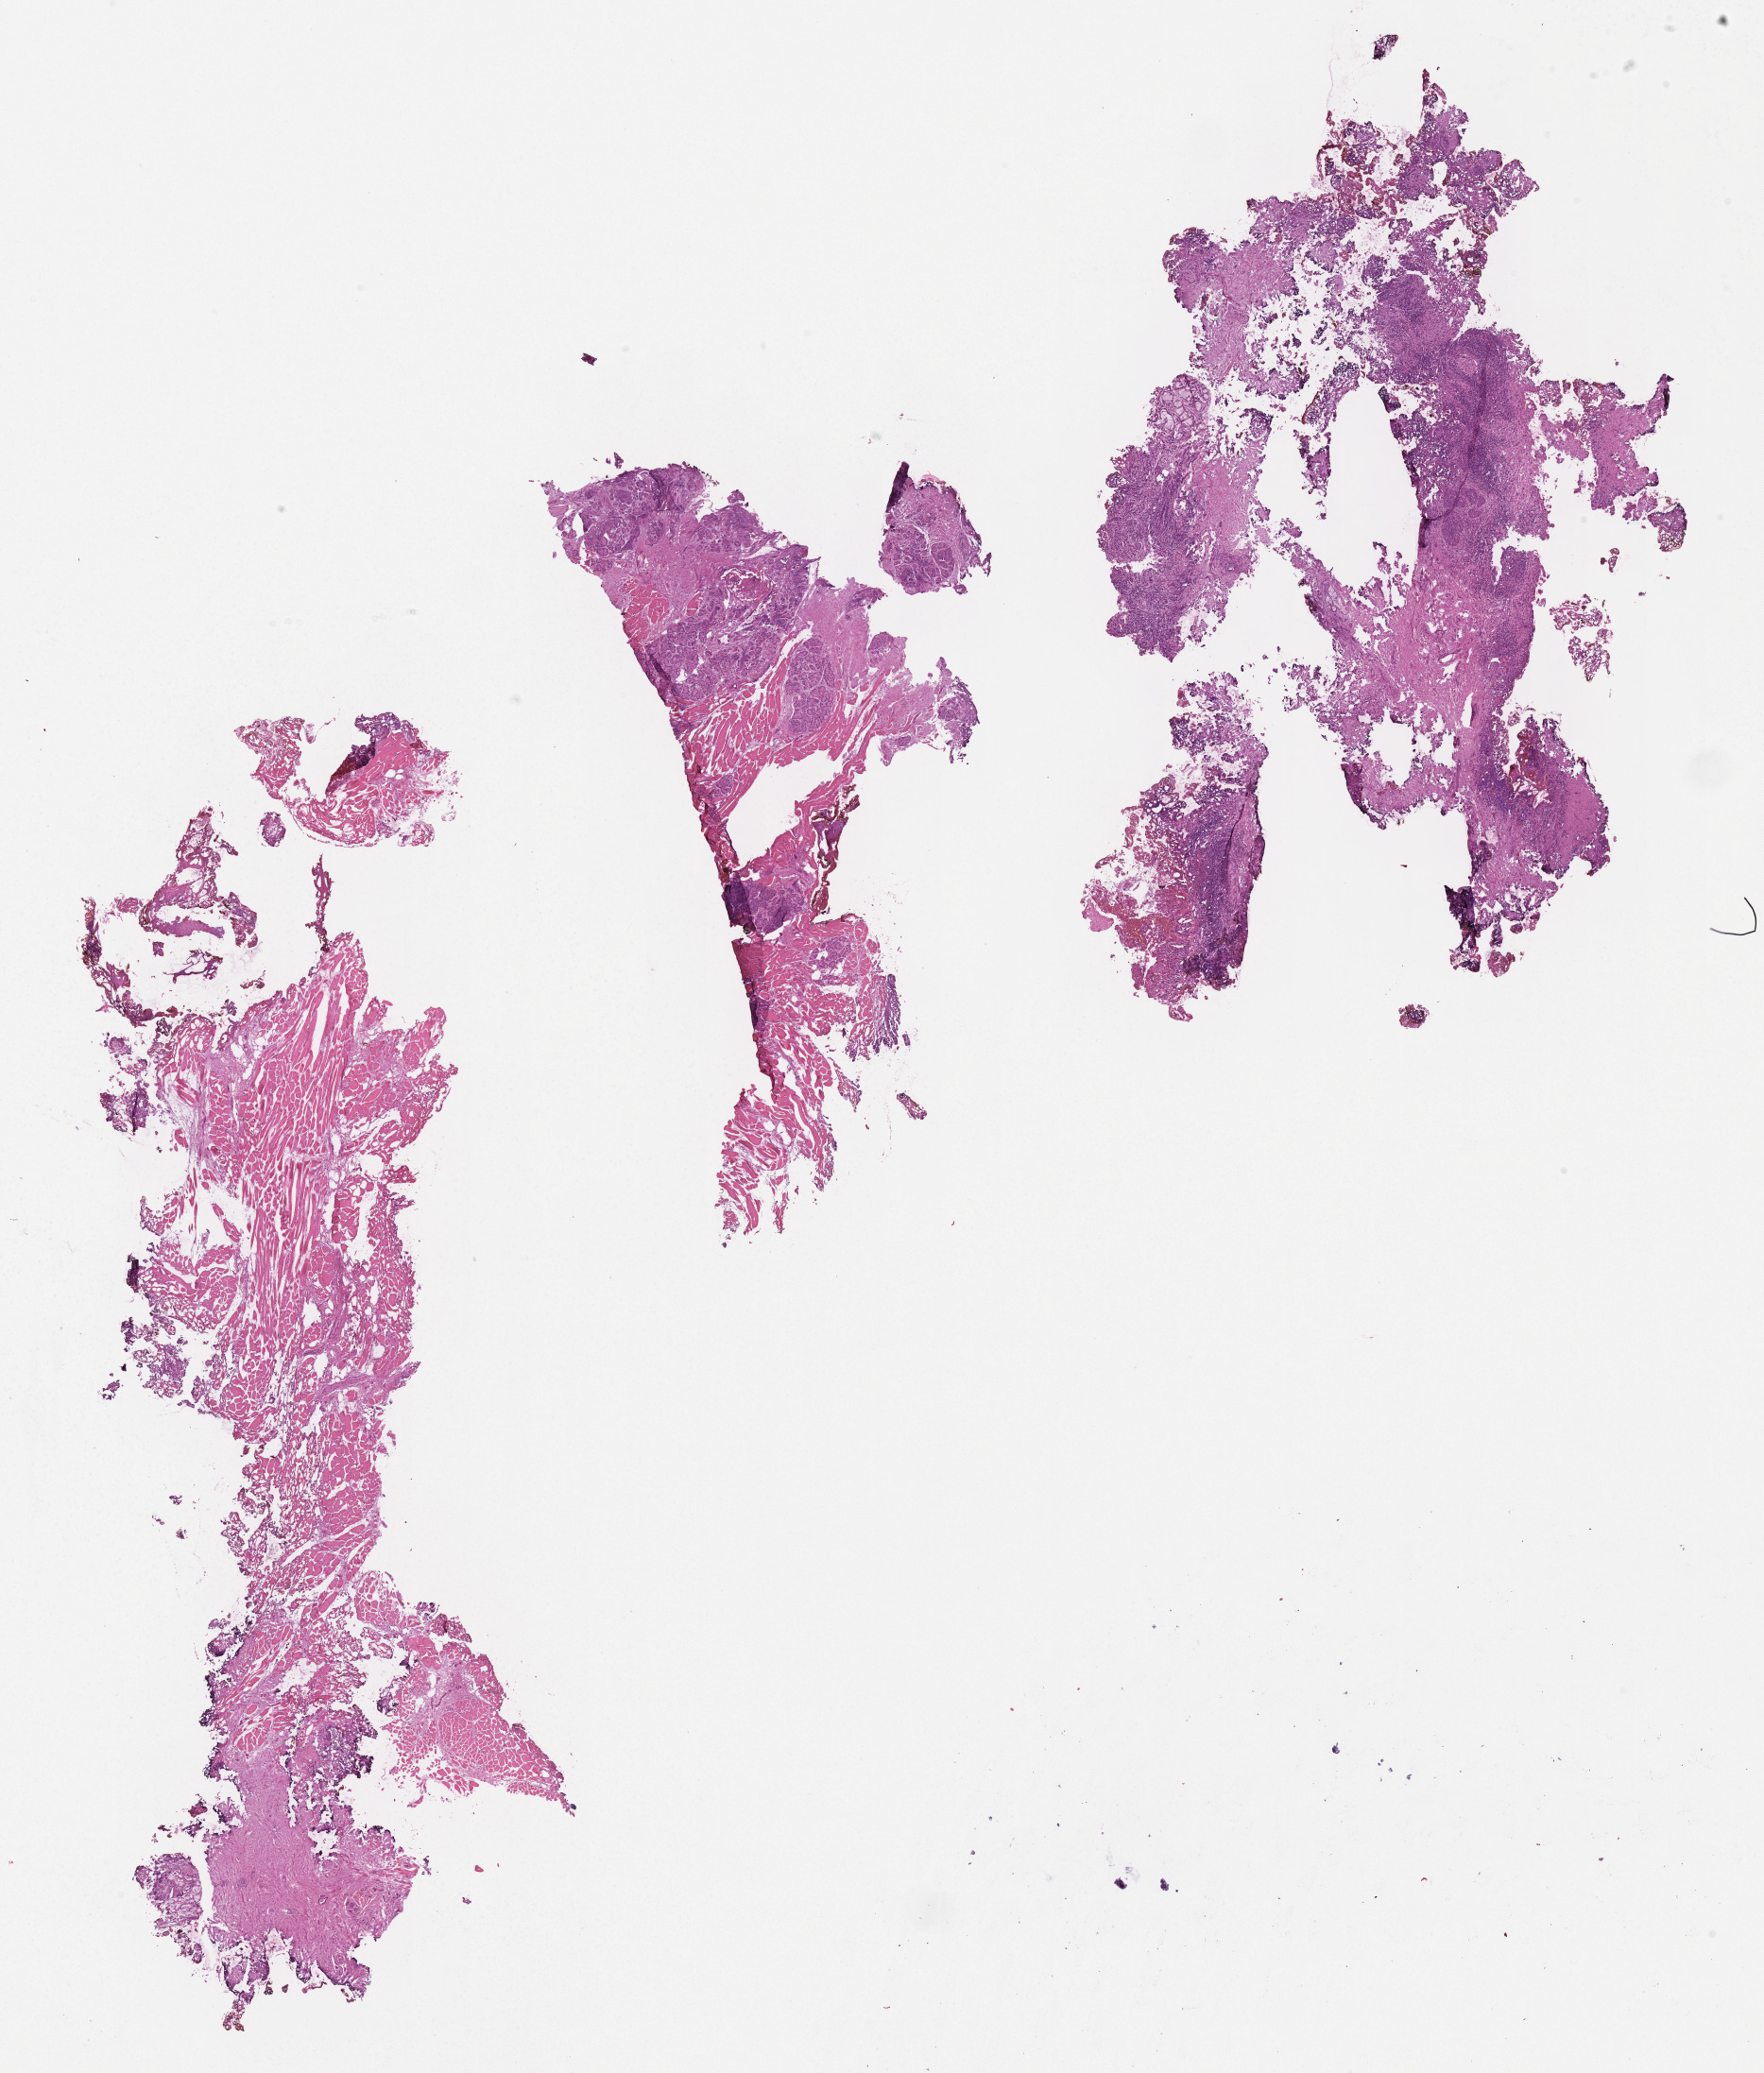
Whole-slide histology image, Hematoxylin and eosin (H&E) stained, low-resolution overview of the scanned area, about 15.1 x 17.7 mm (from a 40x scan); FFPE section; head and neck, primary tumour sample. Male, age 51 years at initial diagnosis.
• pathologic diagnosis: Squamous cell carcinoma, NOS (base of tongue, NOS)
• AJCC pathologic stage: IVA (7th edition)
• TNM: T3 N2b MX